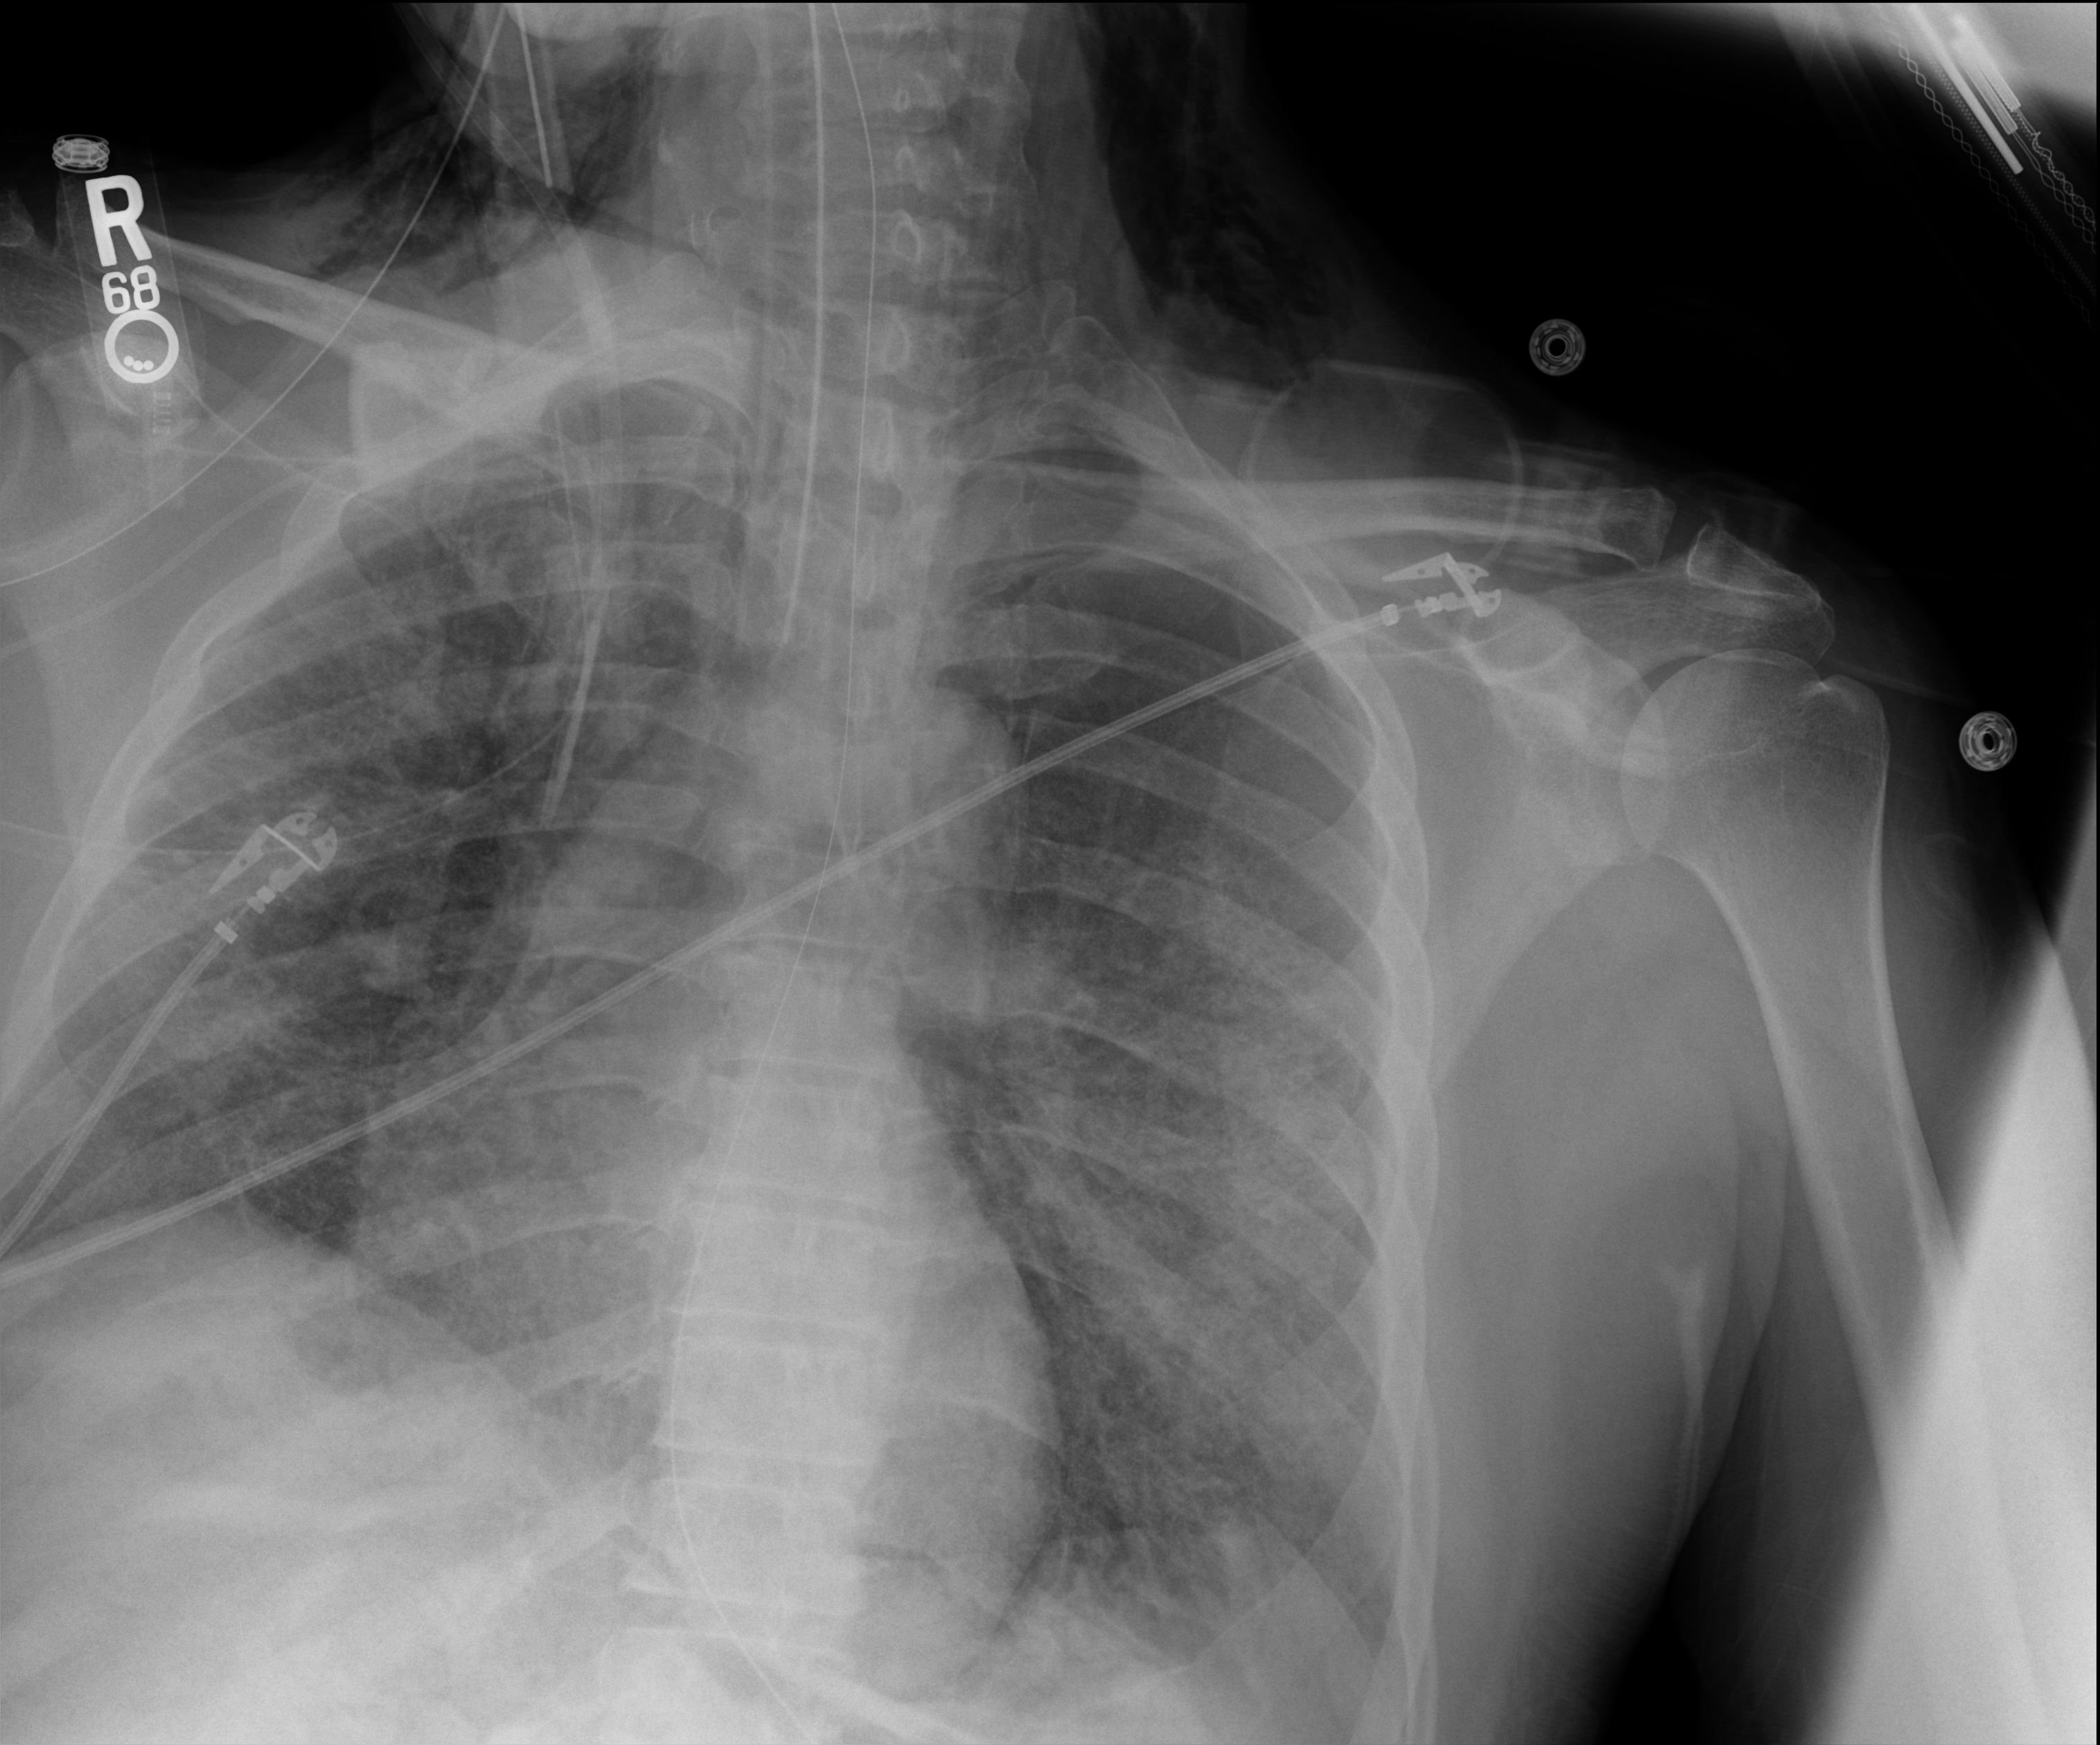
Bedside chest radiograph (digital radiography), anteroposterior (AP) projection. Male patient hospitalised with COVID-19, age 18–59 years.
Admission-level facts for this patient (not findings on this image; timing relative to this image not recorded): diabetes (admission record): no; mechanically ventilated during this hospital stay: yes.